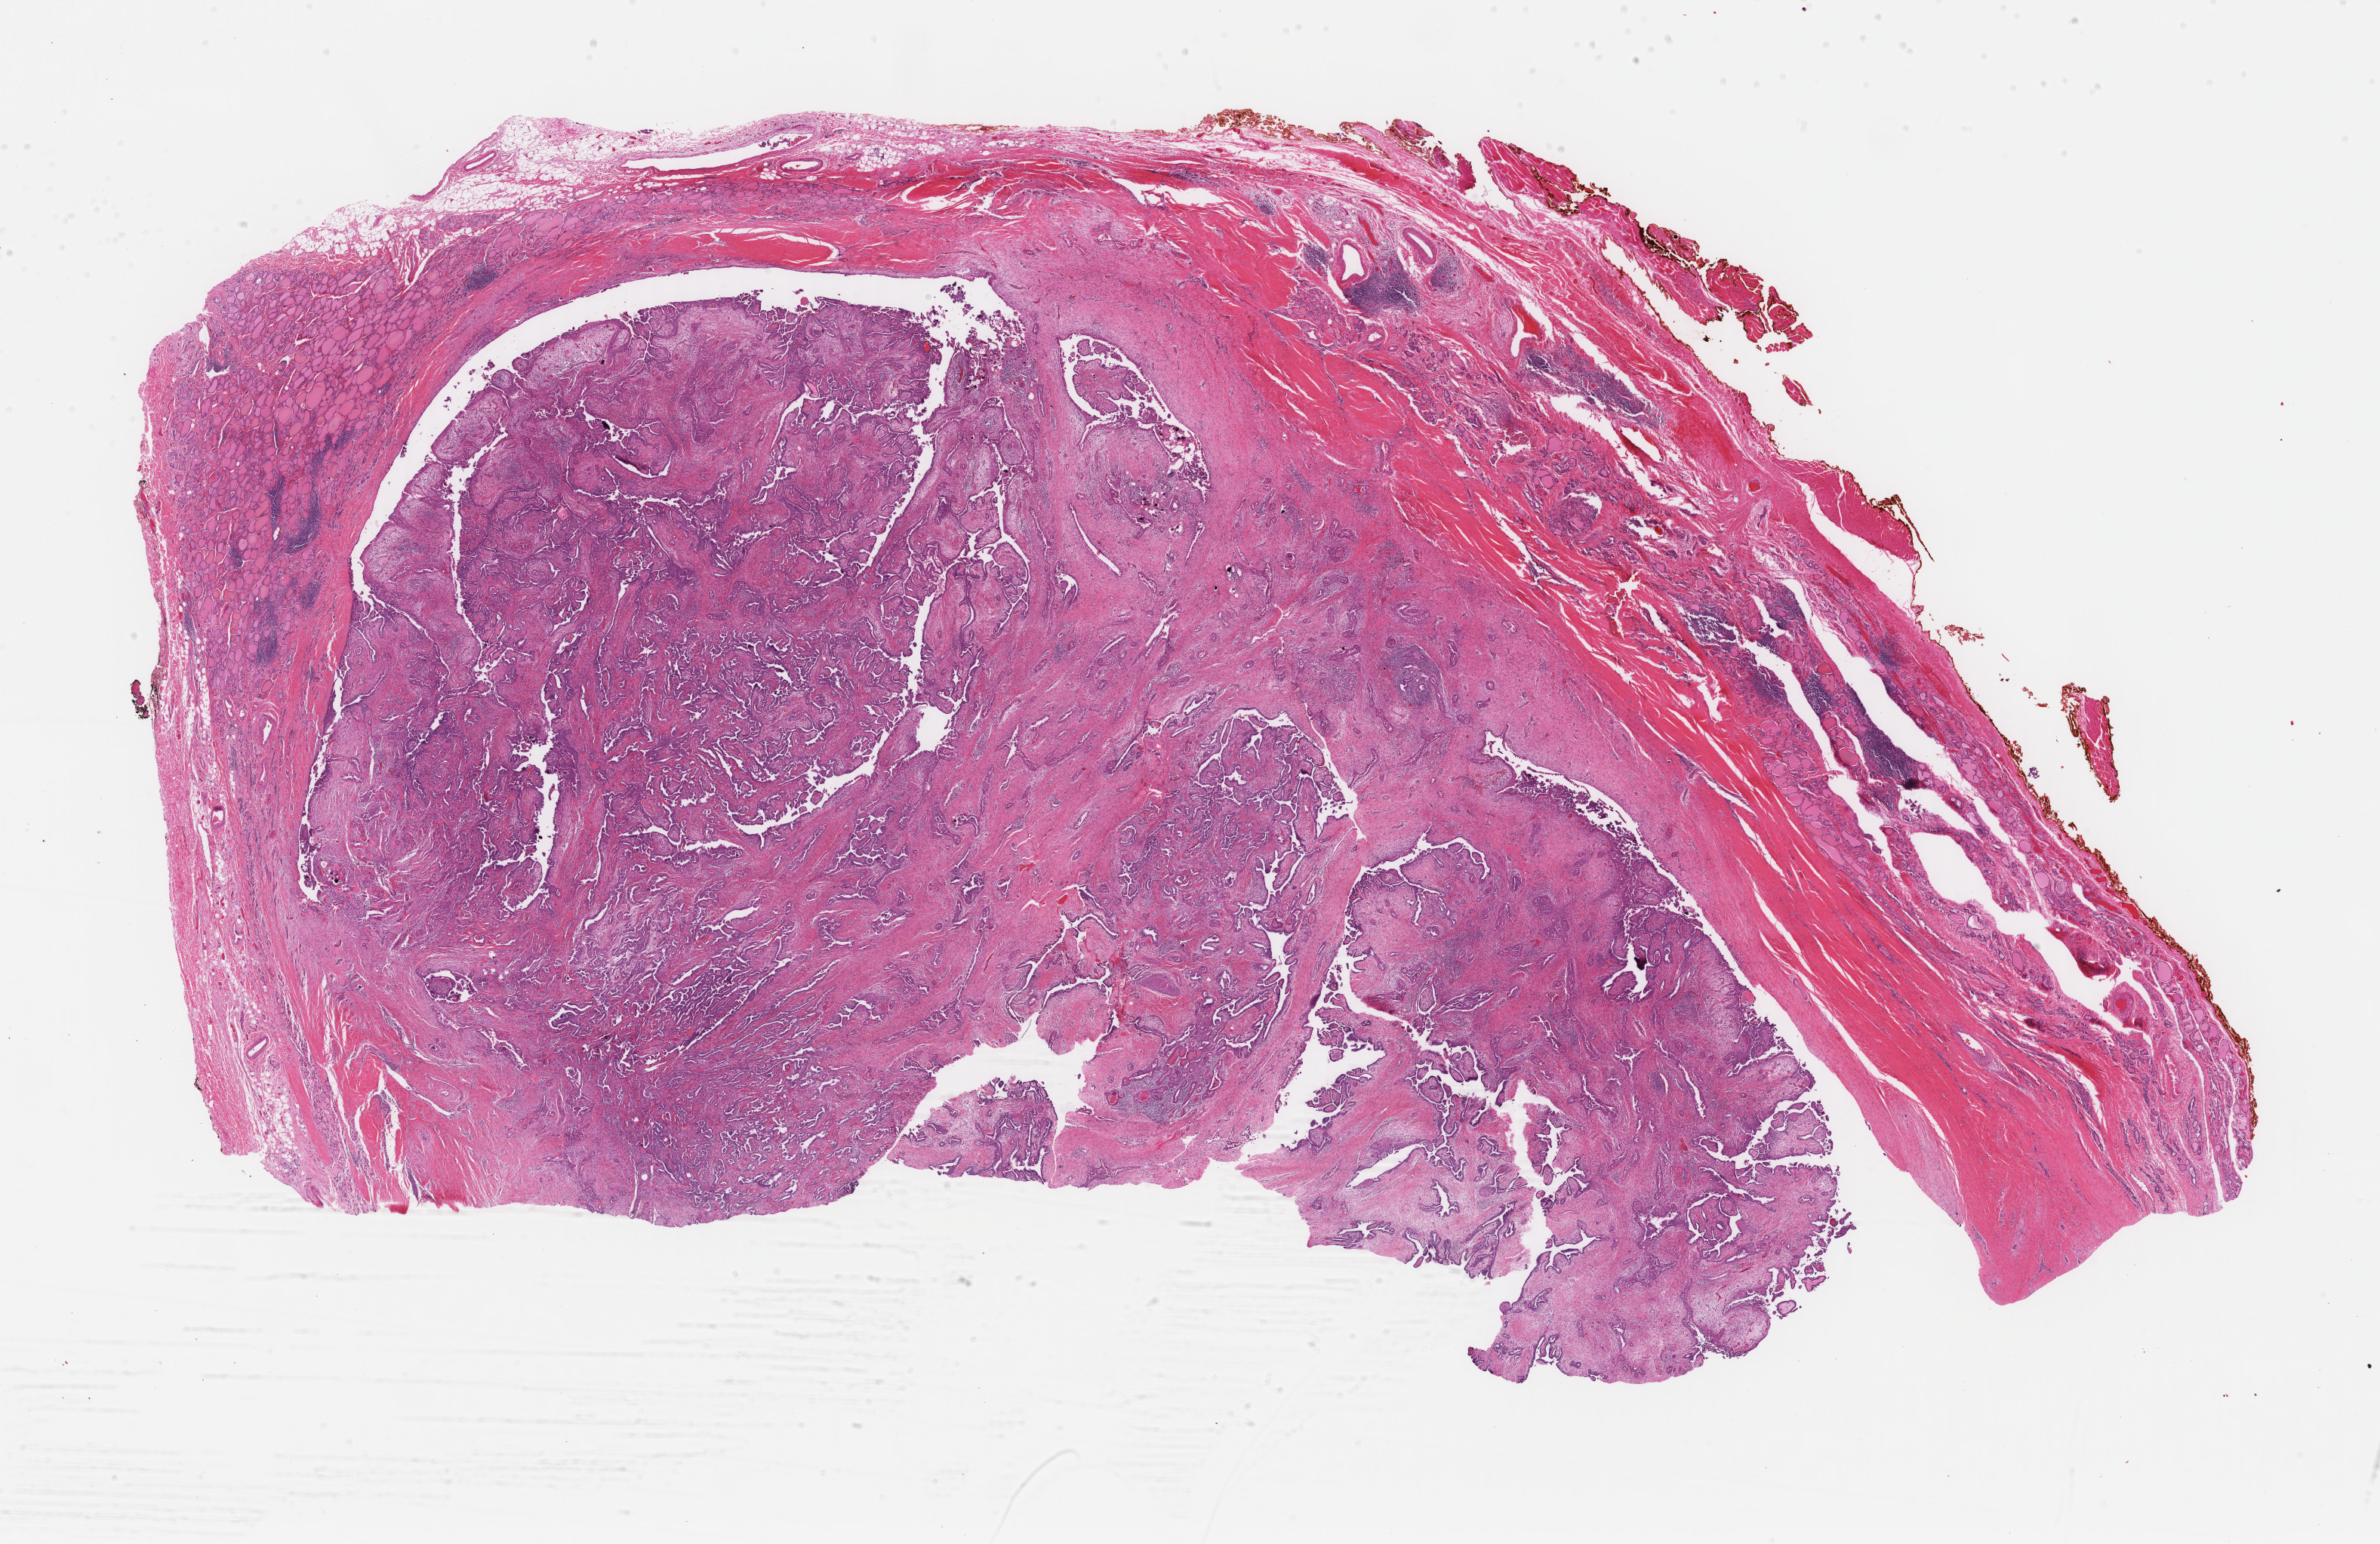
Whole-slide histology image, H&E — shown as a low-resolution overview of the whole scanned area (about 25.0 x 16.2 mm, from a 40x scan); formalin-fixed paraffin-embedded (FFPE) diagnostic section; primary tumour sample from the thyroid. Patient: female, age at initial diagnosis 47 years.
AJCC pathologic stage: III (6th edition). Histologic diagnosis: Papillary adenocarcinoma, NOS (thyroid gland). Lymph nodes positive (case pathology): 2 of 17 examined.